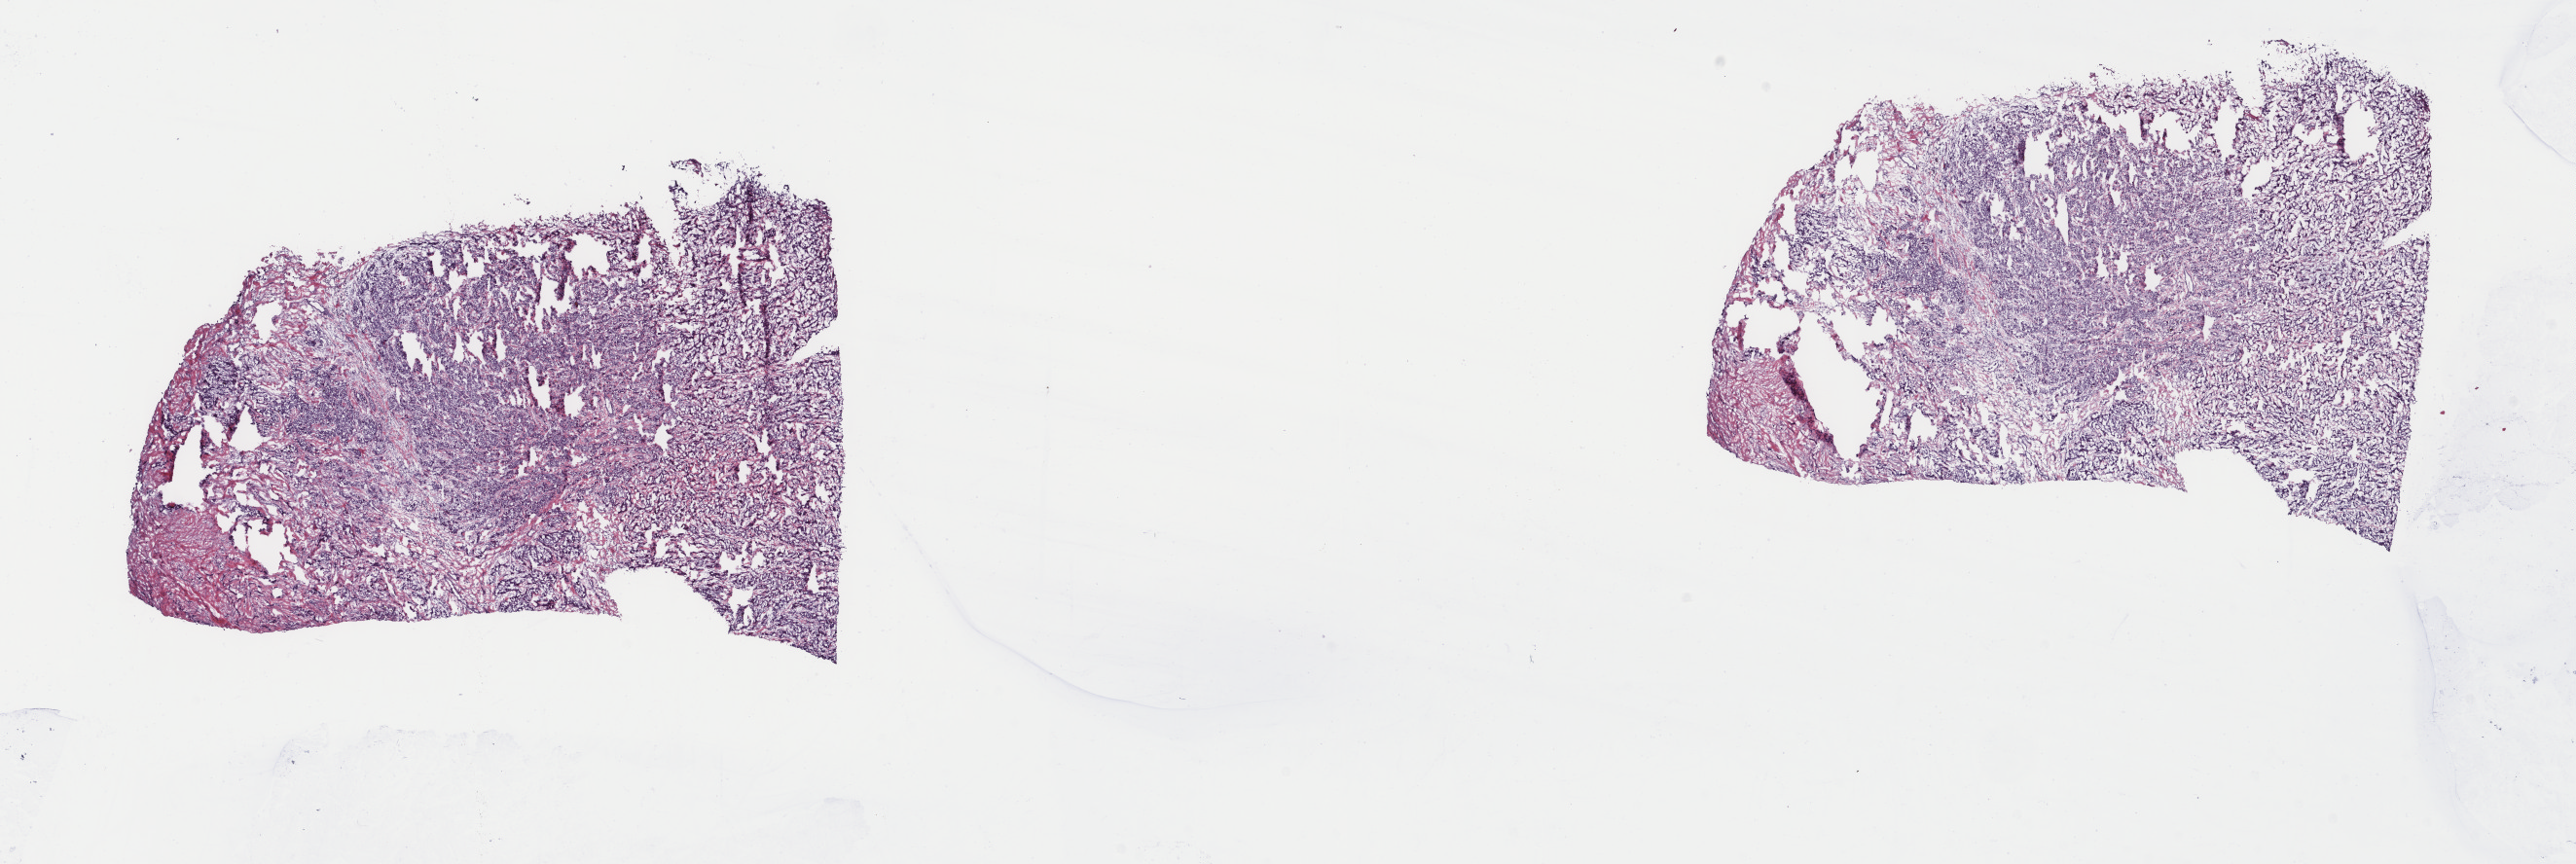
Digitized Hematoxylin and eosin (H&E) stained tissue section (whole slide), shown as a low-resolution overview of the whole scanned area (about 21.0 x 7.0 mm, acquisition: 40x scan). Frozen section from the top of the tissue portion. Sample: primary tumour, liver. Male, age 25 years at initial diagnosis. Histologic grade: G2 (moderately differentiated). Composition of this section per pathologist review: tumour cells 90%, tumour nuclei 75%, normal cells 0%, stromal cells 10%, necrosis 0%. Inflammatory infiltration, as recorded: lymphocyte infiltration 2%, monocyte infiltration 0%, neutrophil infiltration 0%.
Diagnosis: Hepatocellular carcinoma, fibrolamellar. AJCC pathologic stage: I (7th edition).